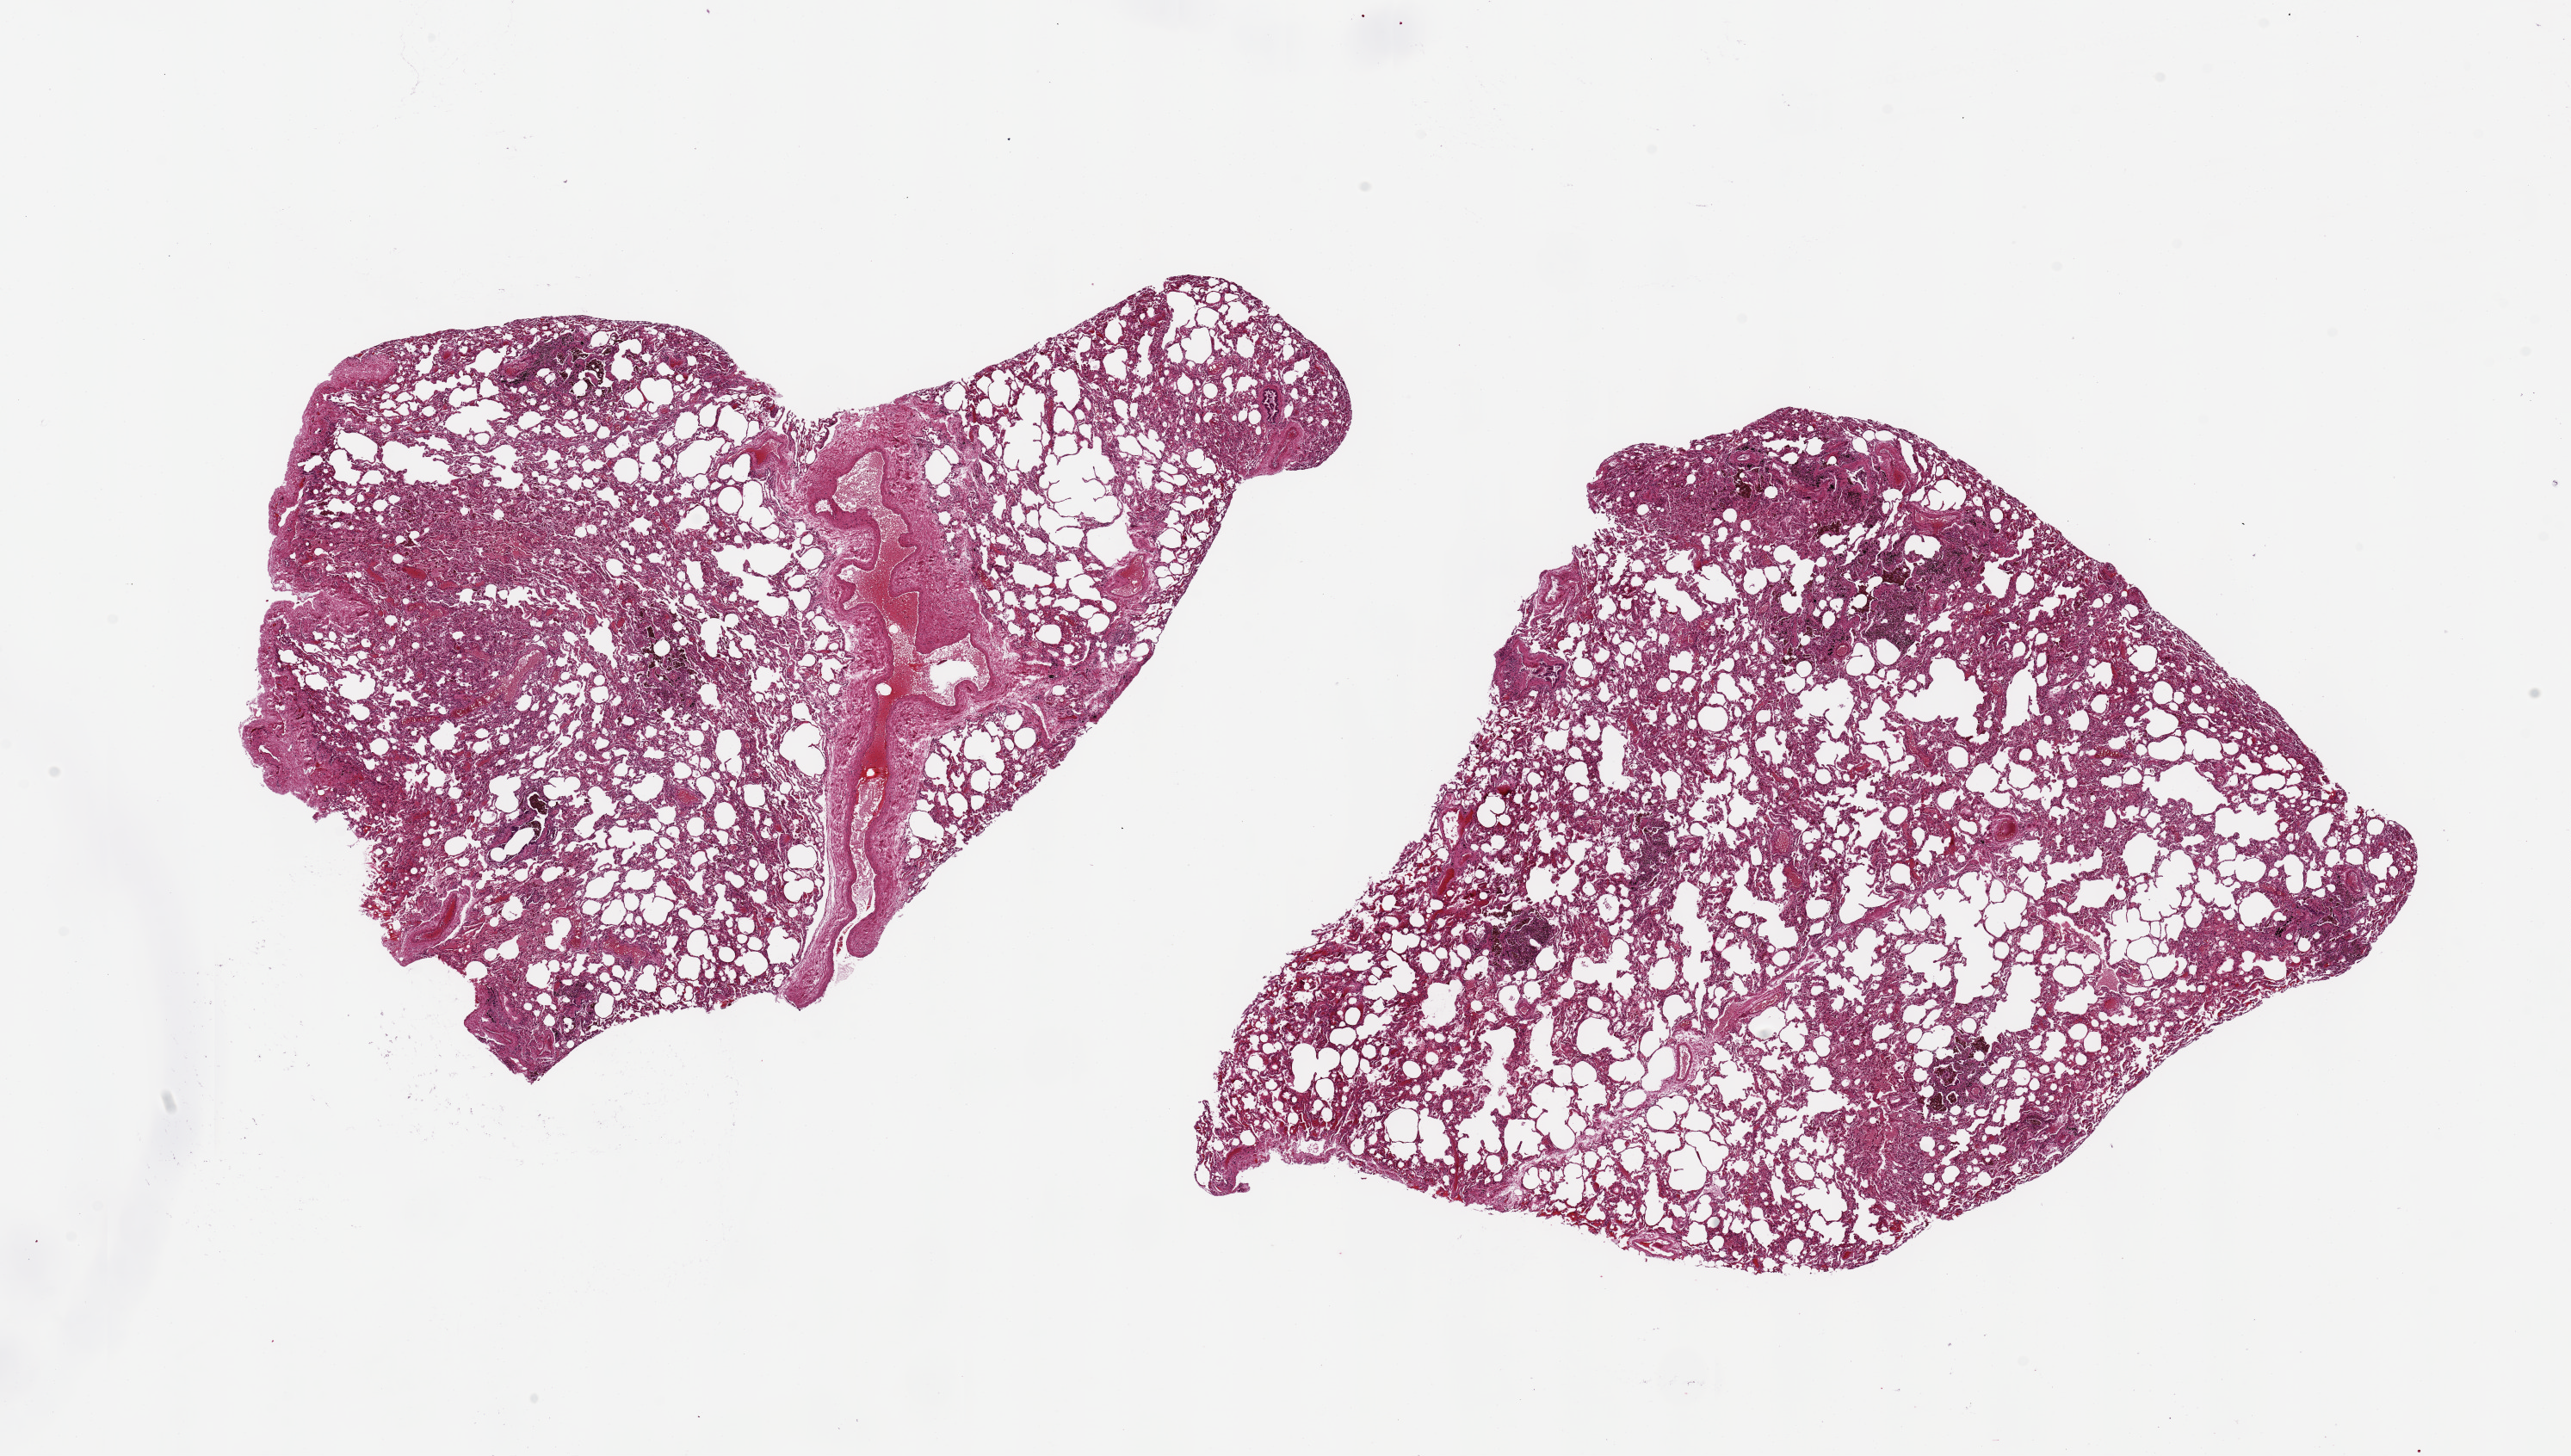
Whole-slide image, H&E stain — a low-resolution overview of the entire scanned area, about 23.6 x 13.4 mm (from a 20x scan), PAXgene-fixed paraffin-embedded (PFPE) section, target tissue: lung, tissue donor sample. Male donor.
- reviewer comment on this tissue sample: 2 pieces up to 9.6x7 mm; focal hemorrhages, anthracotic pigment focally